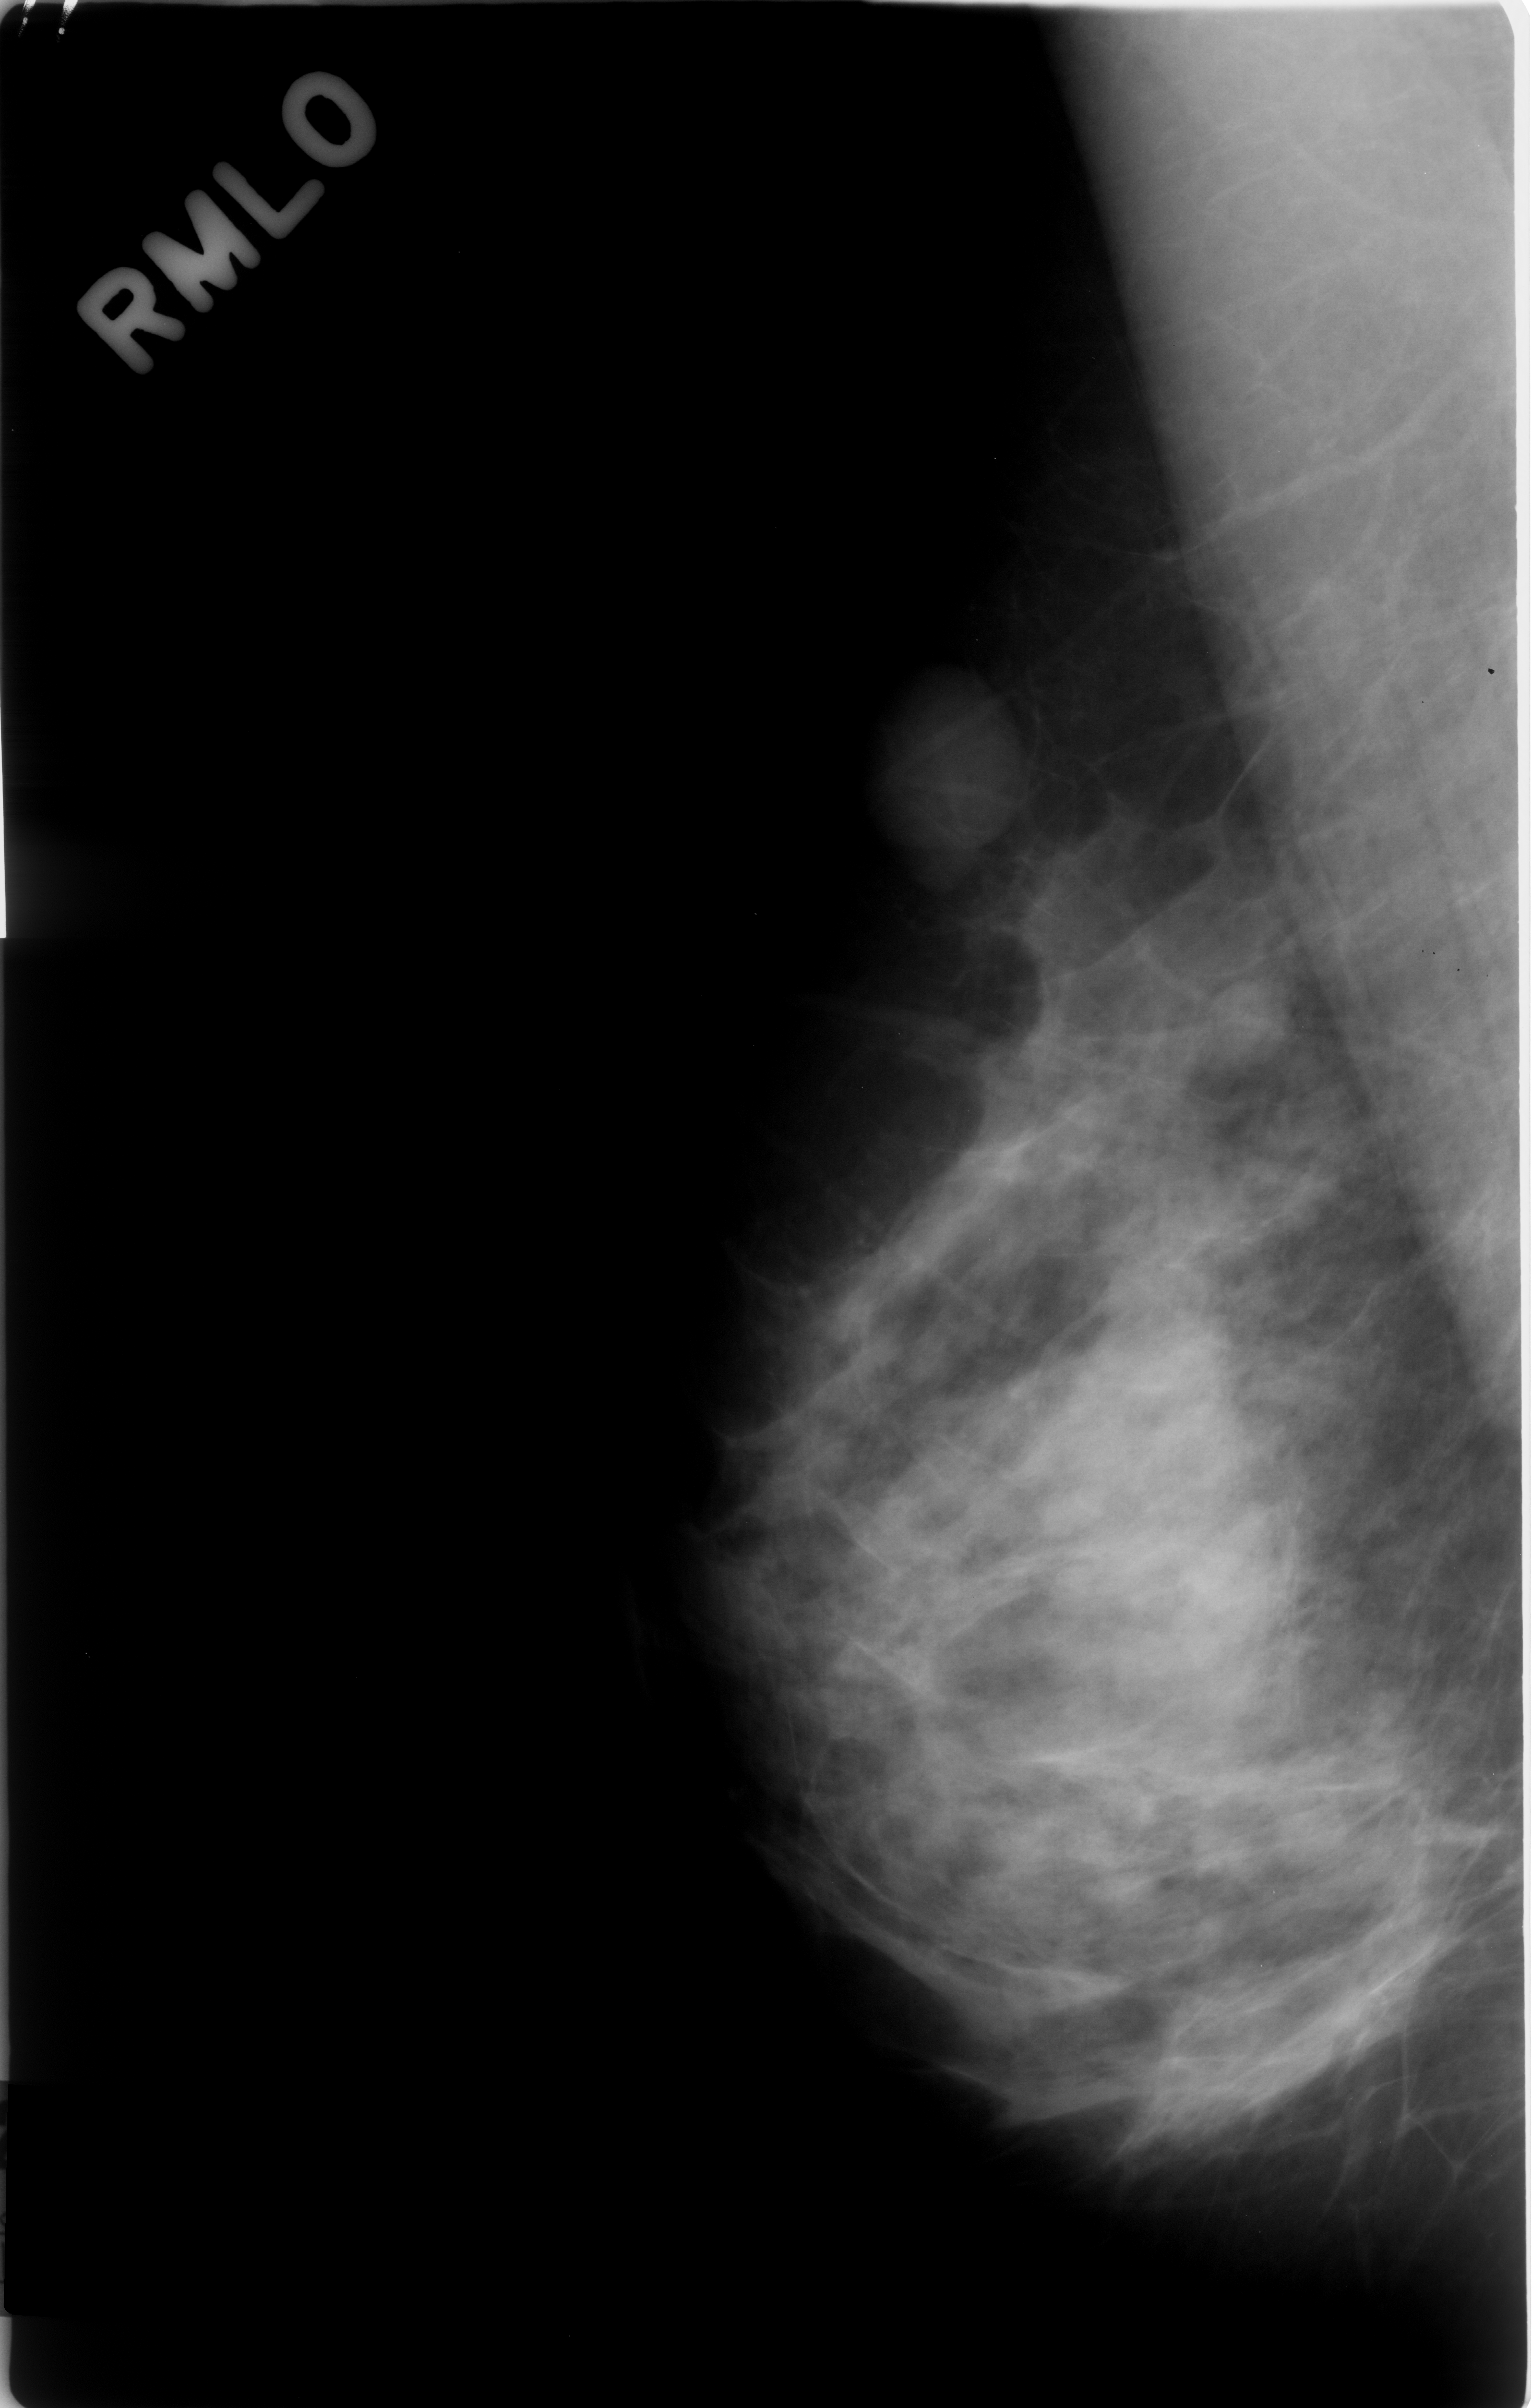
Mammogram (digitized film). Right breast. Mediolateral oblique (MLO) view. BI-RADS breast density category 3 (scale 1–4). 1532 × 2408 image matrix.
Marked abnormalities (boxes around the expert regions of interest):
- mass, shape lobulated, margins circumscribed; BI-RADS assessment category 3; subtlety rating 4 on a 1 (subtle) to 5 (obvious) scale; pathology (as recorded): benign: bounding box (x1, y1, x2, y2) in pixels: (868, 717, 1029, 885)